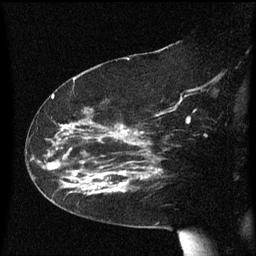
Breast MRI (dynamic contrast-enhanced), one sagittal slice; position 36 of 60 along the scan axis; dynamic contrast-enhanced series, image 2 of 3 at this slice position (ordered by acquisition); 1.5 T; TE 4.2 ms, TR 8.4 ms; 256 × 256 image matrix. Patient: female, 63 years. From the clinical record (not read from this slice): setting: breast cancer imaged before/during neoadjuvant chemotherapy; receptor status: HER2-positive.
Outlined on this slice (semi-automatically segmented with operator editing):
- analysis volume of interest (the breast-tissue region the enhancement analysis was run in; not a lesion): bounding box <71,144,147,197> (left, top, right, bottom; pixels)
- tumour enhancement mask (voxels above the 70 % enhancement threshold inside the analysis volume of interest): <94,168,147,193>